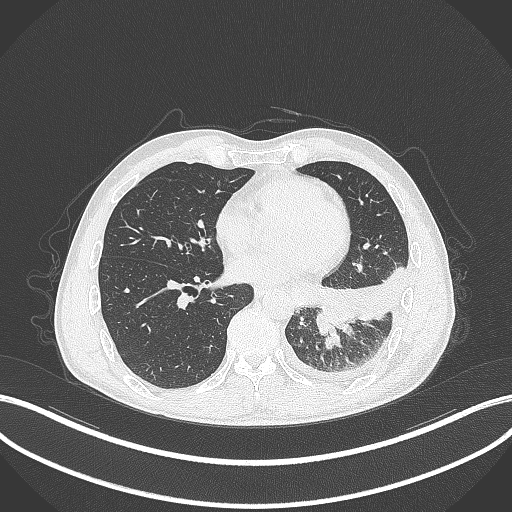
Chest CT, one axial slice; position 122 of 295 along the scan axis; reconstruction kernel B70f; lung window (W 1500 / L -600 HU); 1 mm slice thickness; 512 × 512 image matrix, field of view 400 × 400 mm. Male patient, age 47 years. From the clinical record (not read from this slice): clinical TNM (as recorded): T3 N1 M1c; histopathological grade: G3.
Outlined on this slice (bounding box drawn by a radiologist):
- lung tumour (recorded histology: small cell carcinoma): bounding box (x1, y1, x2, y2) in pixels: (313, 302, 357, 337)